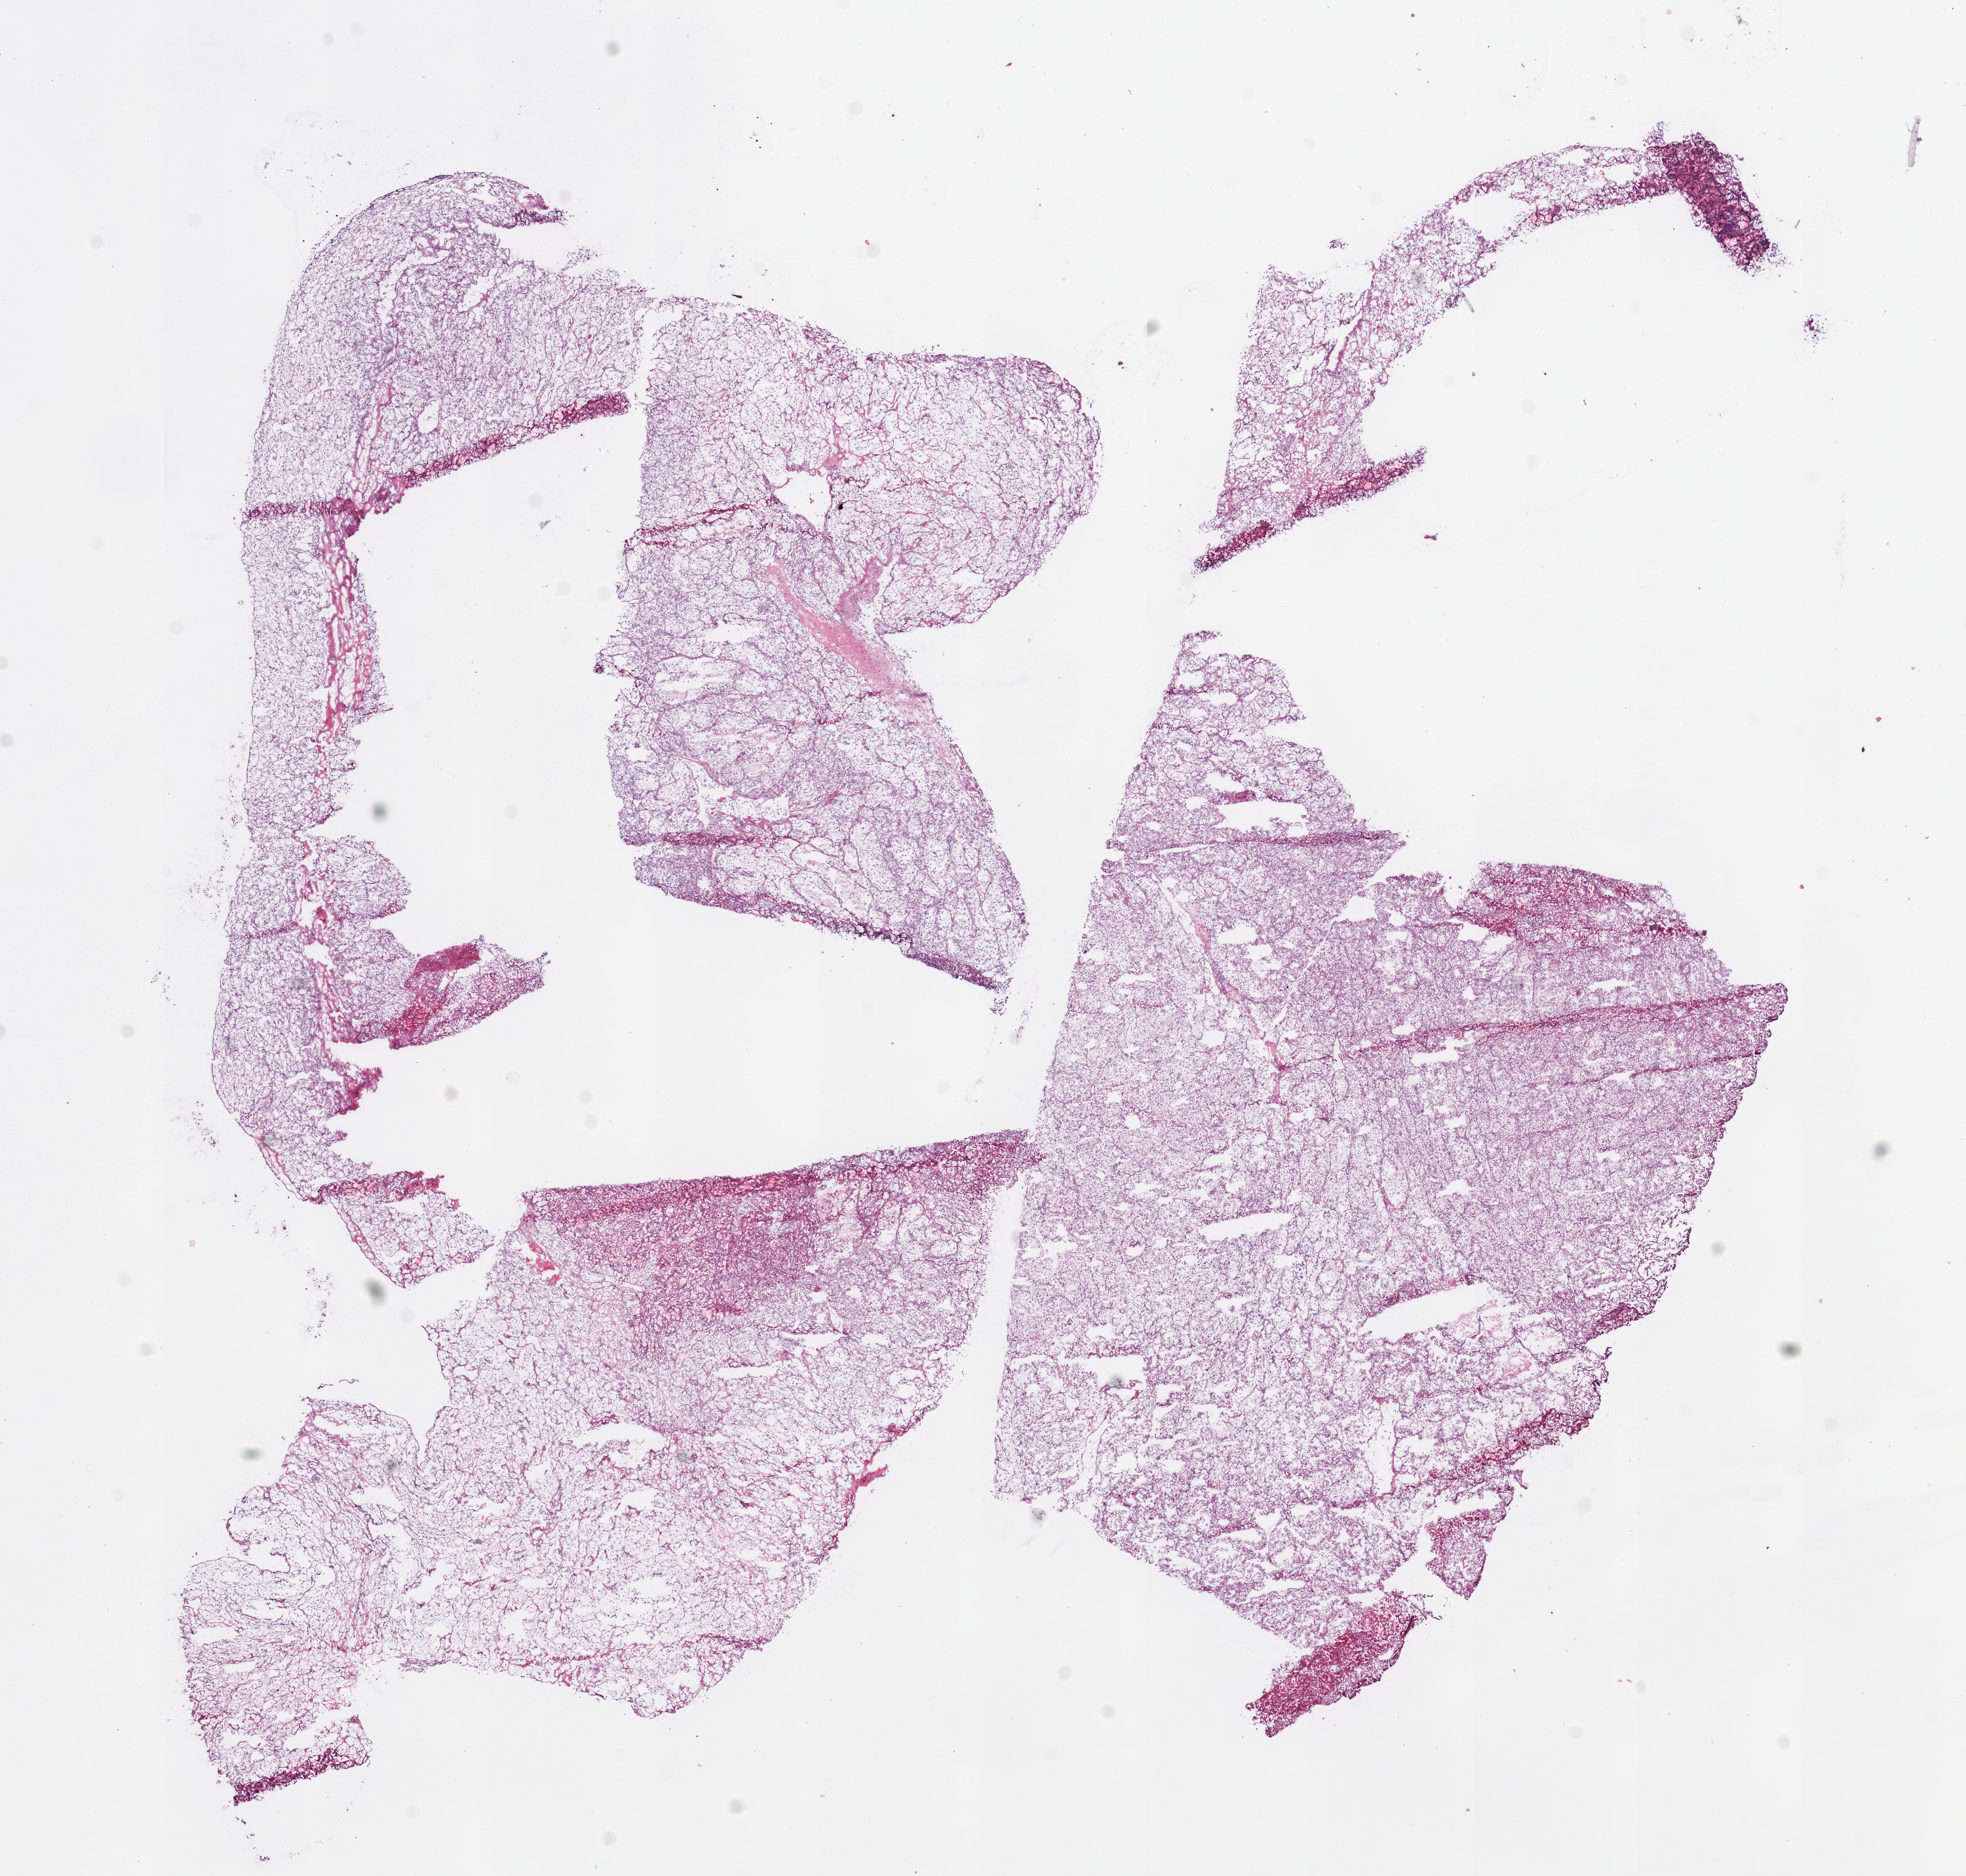
H&E-stained whole-slide image — a low-resolution overview of the entire scanned area, about 12.0 x 11.5 mm (from a 20x scan). Frozen section from the bottom of the tissue portion. Kidney, primary tumour sample. Female, age 71 years at initial diagnosis.
Diagnosis: Clear cell adenocarcinoma, NOS.